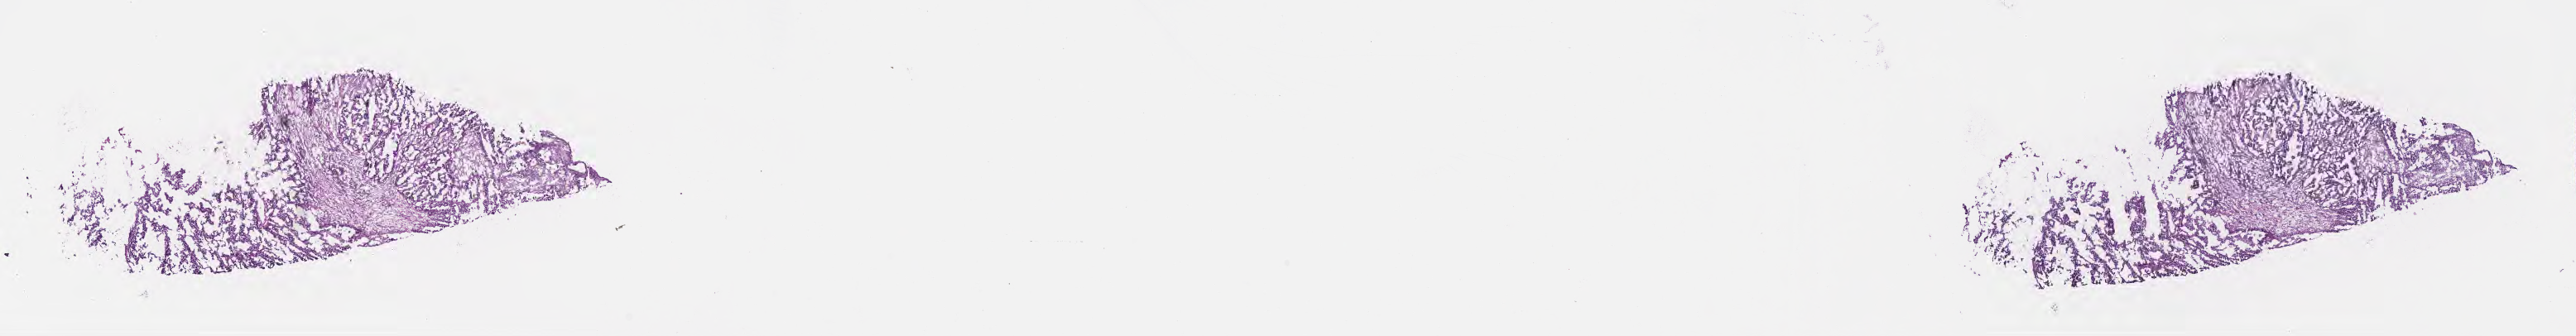
Whole-slide image, haematoxylin and eosin stain — shown as a low-resolution overview of the whole scanned area (about 25.2 x 3.3 mm); frozen section; specimen: primary tumor; site: stomach. Patient: male, age at initial diagnosis 43 years. Pathologist review of this section (percent, as recorded): tumor cells 100%, tumor nuclei 80%, stromal cells 0%, necrosis 0%, normal cells 0%. Infiltration values recorded for this section: lymphocyte infiltration 0%, monocyte infiltration 0%, neutrophil infiltration 0%.
Section: top of the tissue portion. Diagnosis: Adenocarcinoma, NOS.